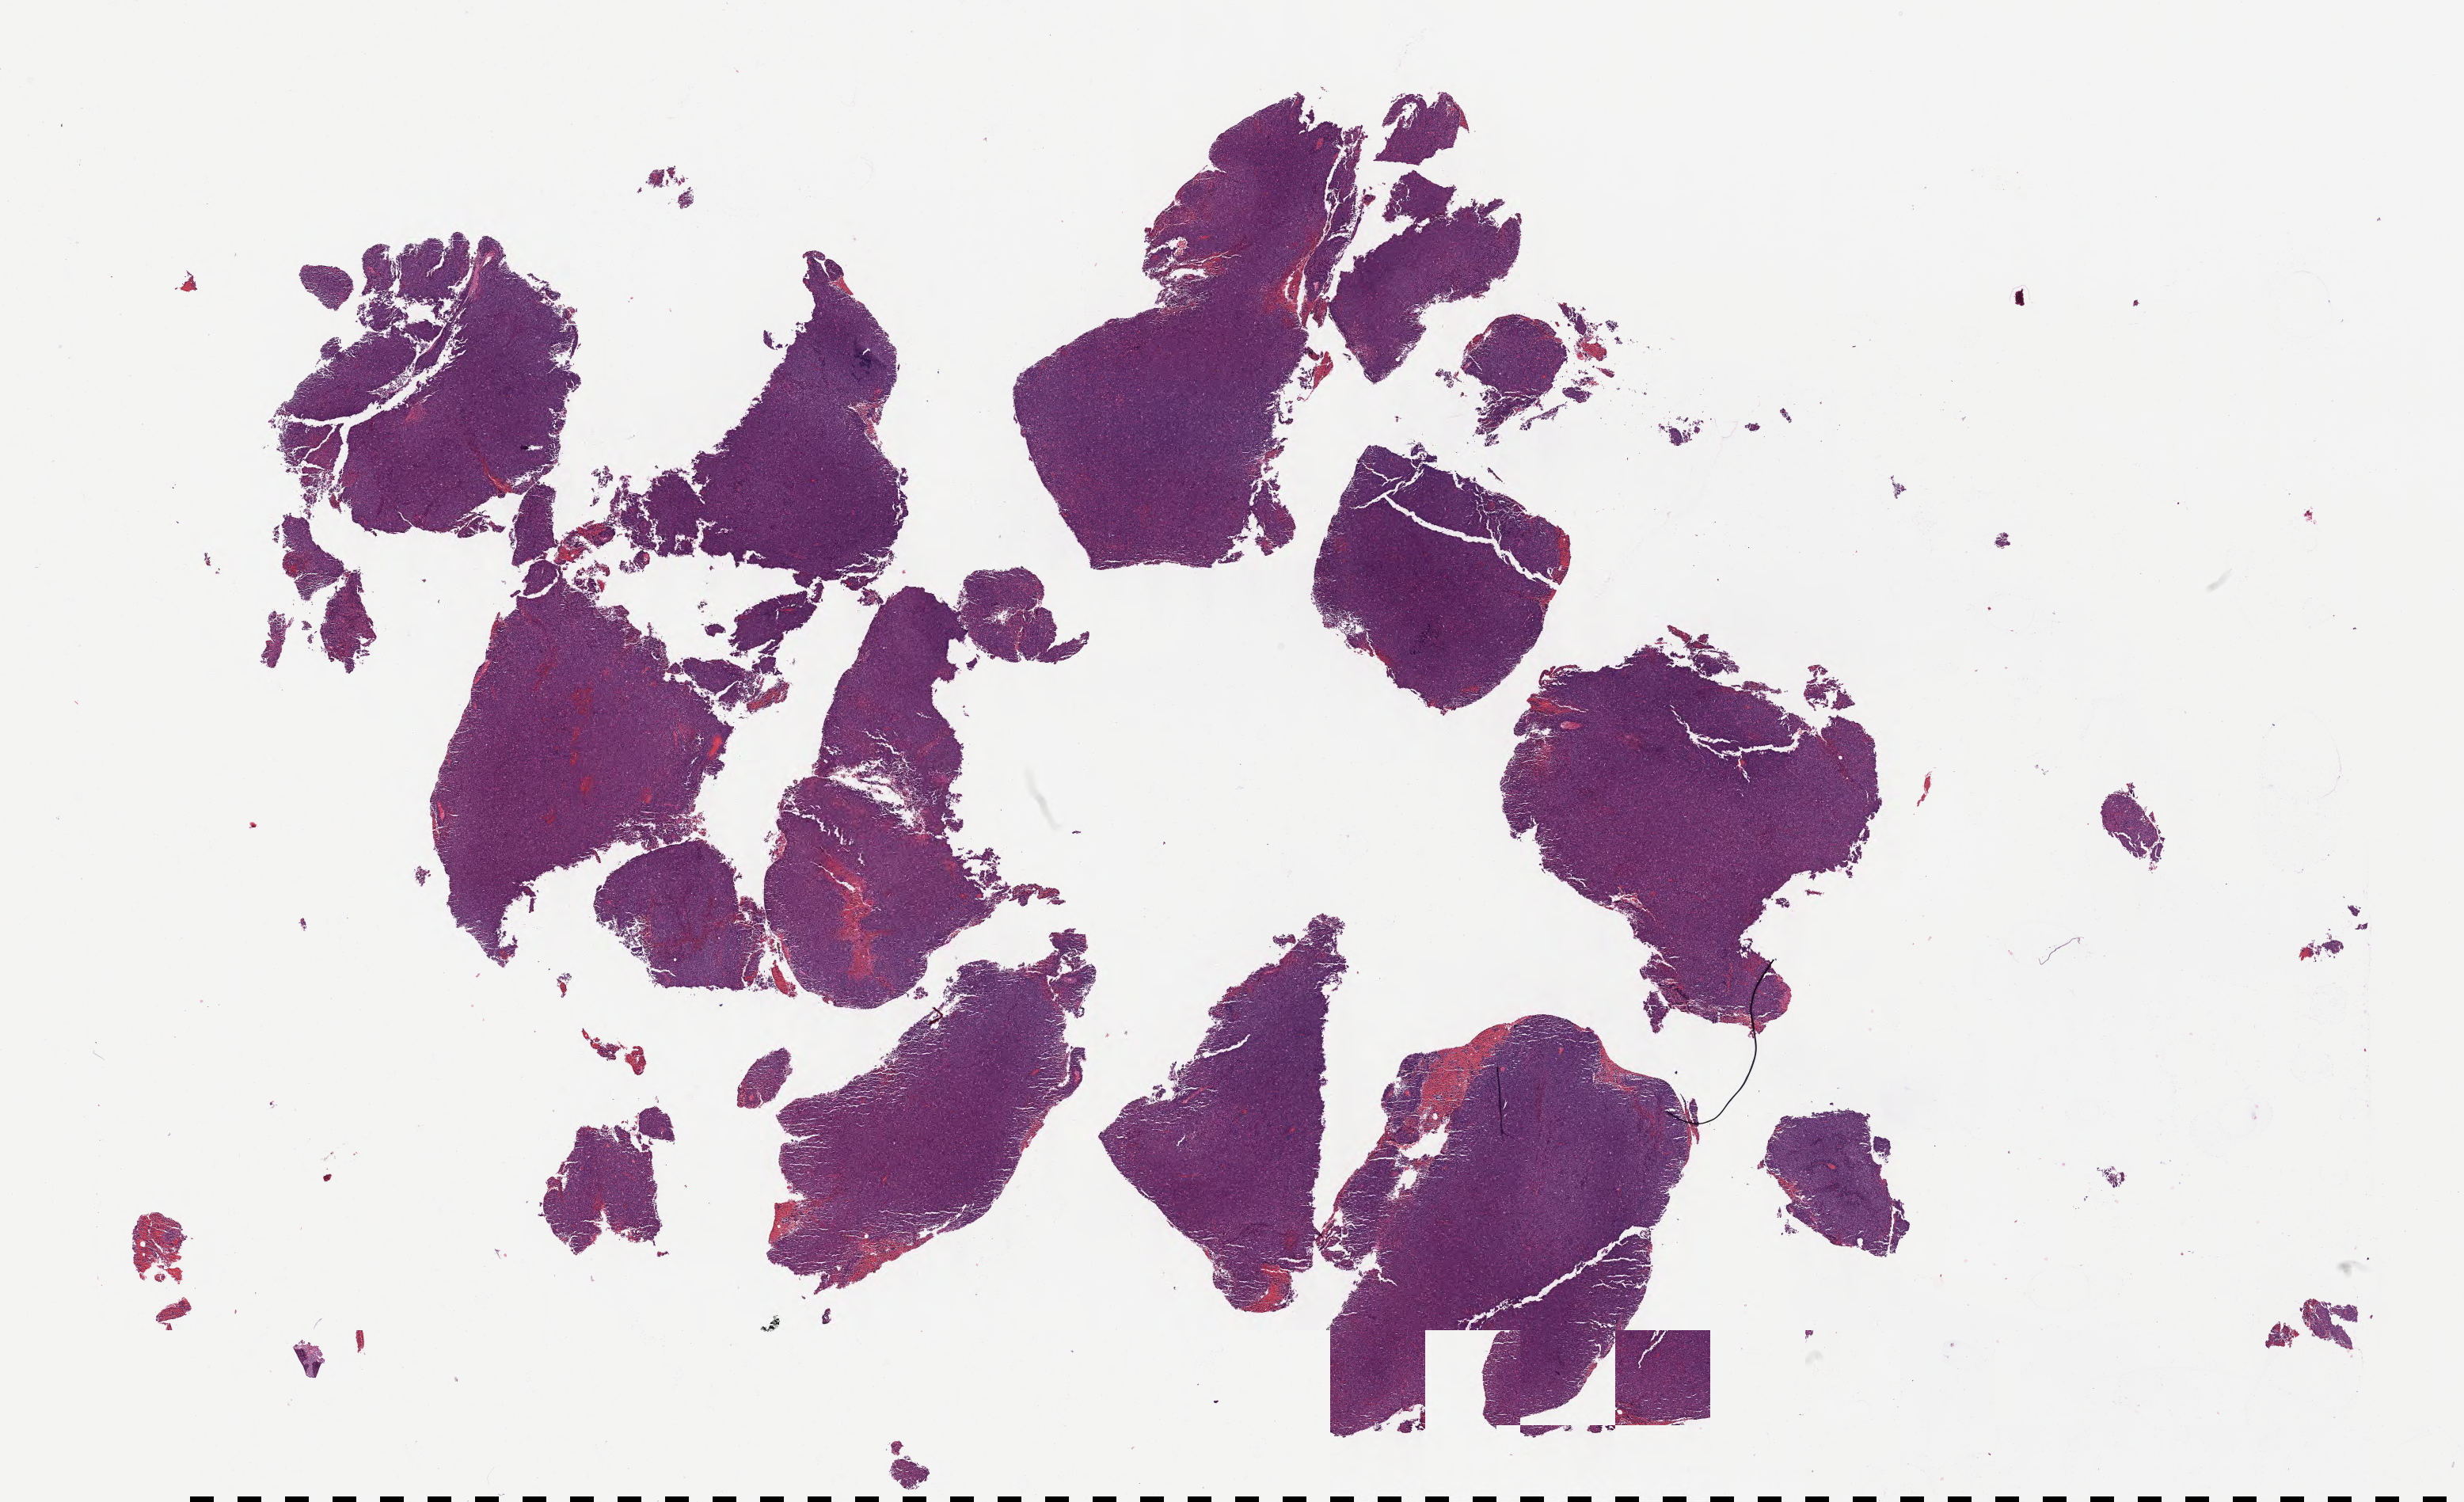
Whole-slide image, haematoxylin and eosin stain — low-resolution overview of the scanned area, about 25.1 x 15.3 mm. Specimen: tumor tissue. Site: lymph node. Patient female; aged 50.
Diagnosis: Diffuse large B-cell lymphoma, NOS.